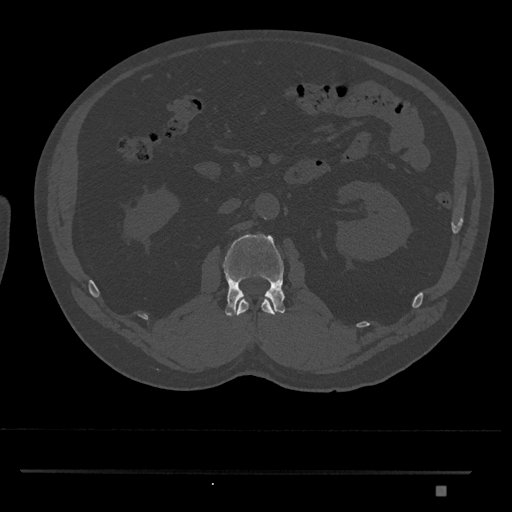
CT including the spine, one axial slice; position 775 of 1134 along the scan axis; bone window (W 1800 / L 400 HU); 0.5 mm slice thickness; 512 × 512 image matrix, field of view 429 × 429 mm. Patient: male, 65 years. Case-level facts recorded for this patient, not image findings: primary cancer: prostate.
Annotated regions visible in this slice (semi-automatic segmentation, software-assisted and operator-edited):
- L1 vertebra: bounding box [x1, y1, x2, y2] px = [237, 298, 275, 316]
- L2 vertebra: [222, 234, 285, 316]